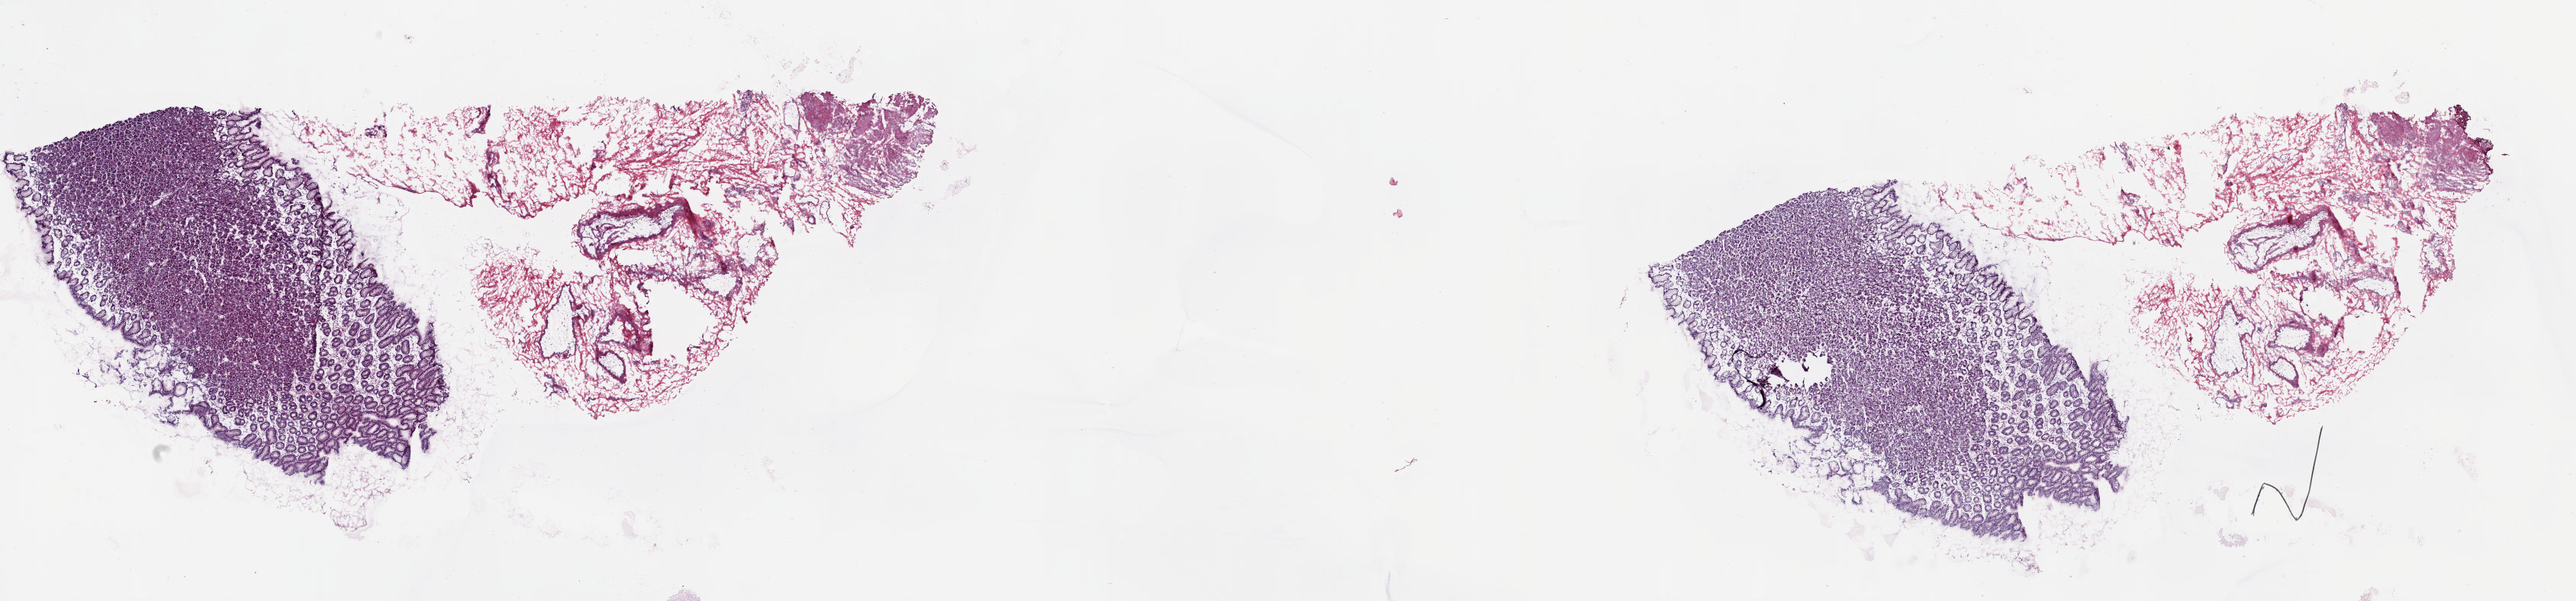
Whole-slide histology image, H&E — shown as a low-resolution overview of the whole scanned area (about 26.8 x 6.3 mm), frozen section from the top of the tissue portion, solid tissue normal (non-tumour tissue) sample from the esophagus. Patient: male, age at initial diagnosis 60 years. Pathologist review of this section (percent, as recorded): tumour cells 0%, tumour nuclei 0%, normal cells 100%, stromal cells 0%, necrosis 0%. Infiltration values recorded for this section: lymphocyte infiltration 0%, monocyte infiltration 0%, neutrophil infiltration 0%.
This section: solid tissue normal sample (biorepository sample class). Patient diagnosis: Adenocarcinoma, NOS.